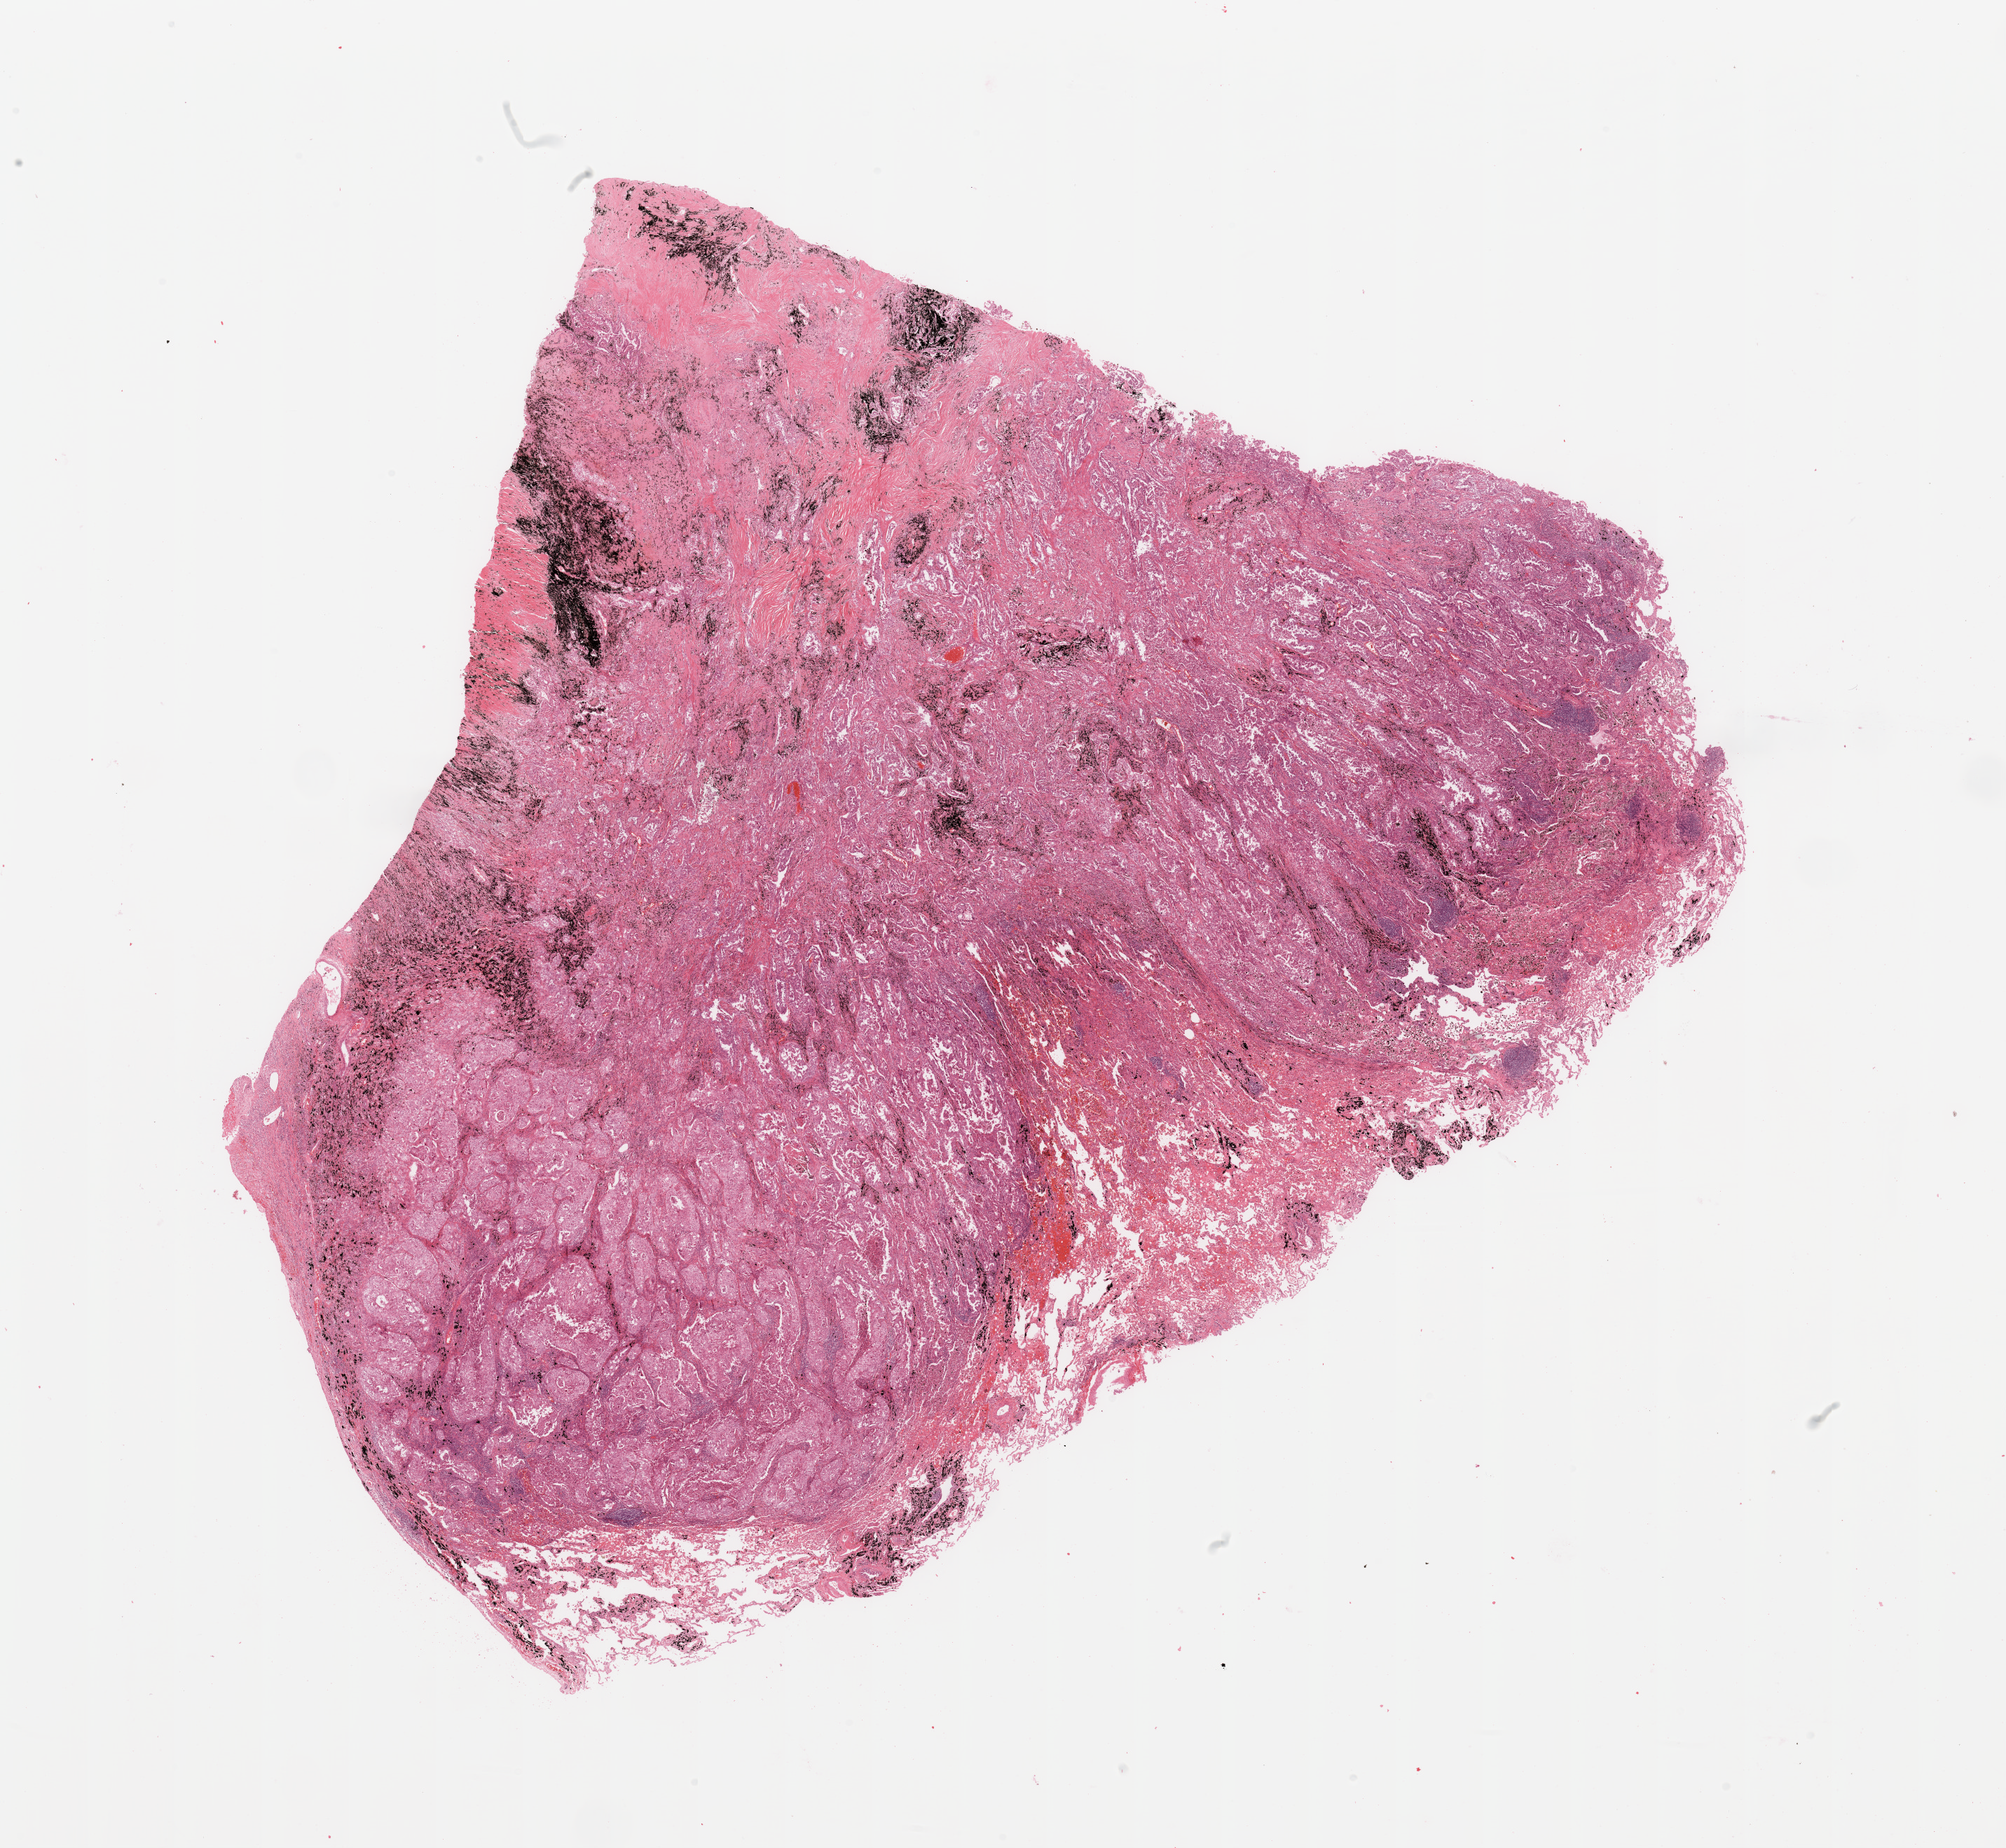
Digitized Hematoxylin and eosin (H&E) stained tissue section (whole slide), whole scanned area (about 22.6 x 20.9 mm, acquisition: 20x scan) shown as a low-resolution overview, lung, tumour tissue. Male, 65 y/o. Histologic grade: G3 (poorly differentiated).
Histologic diagnosis: Adenocarcinoma, NOS. AJCC pathologic stage: IB.